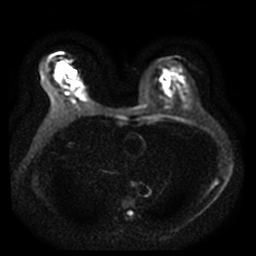
Breast MRI, one axial slice; diffusion-weighted series; image 2 of 4 stored at this slice position (different b-values; order by instance number); 3 T; 5 mm slice thickness; 256 × 256 image matrix, field of view 340 × 340 mm. Female patient.
Outlined on this slice (outlined manually by an expert reader):
- tumour on diffusion-weighted imaging: bounding box [x1, y1, x2, y2] px = [61, 62, 68, 70]